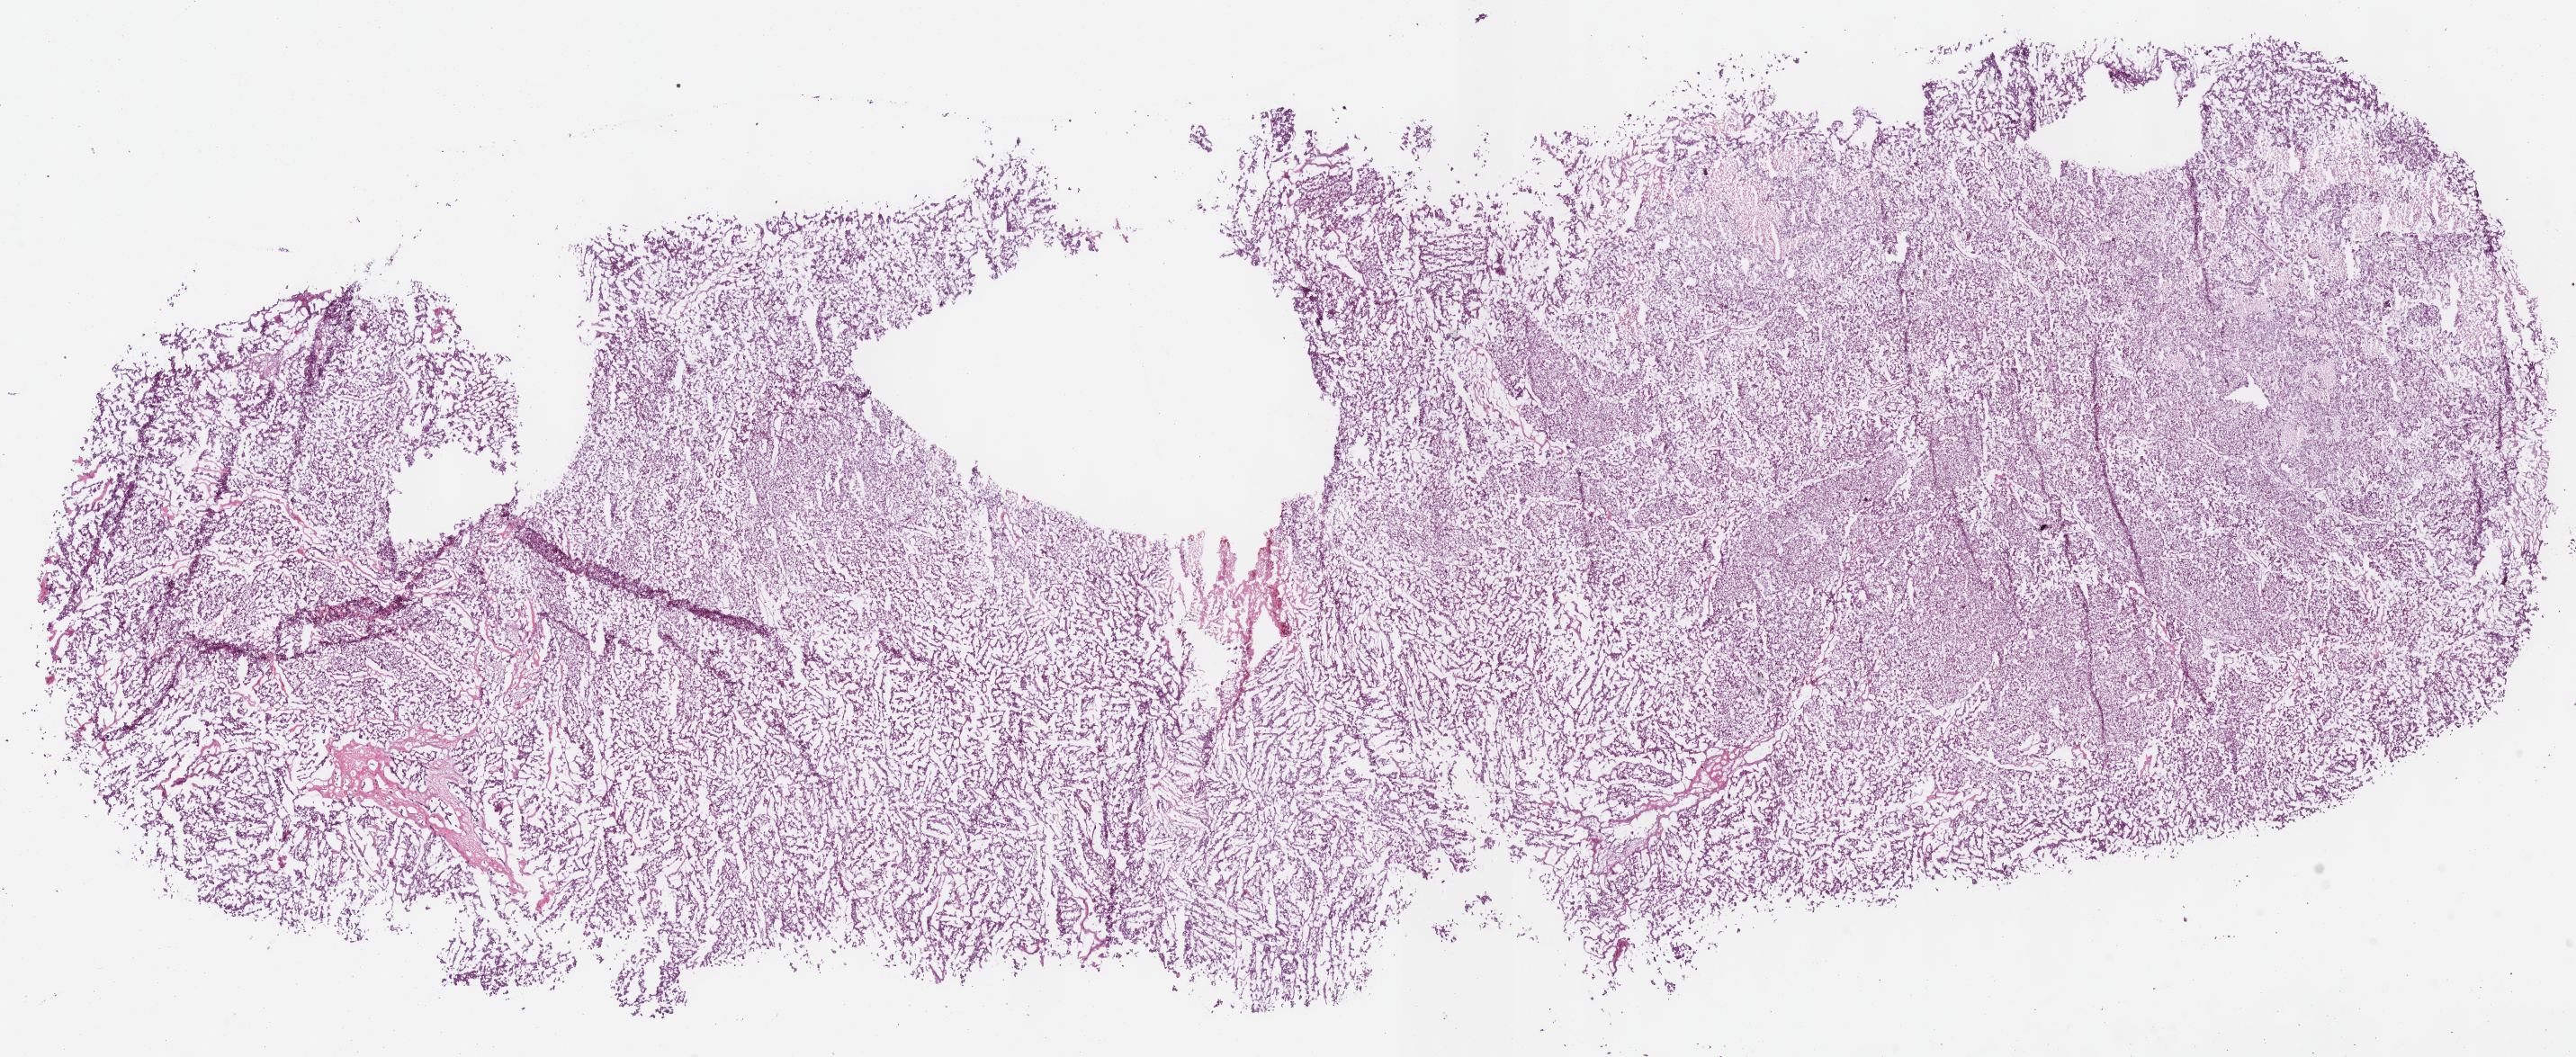
Whole-slide histology image, H&E, whole scanned area (about 22.5 x 9.2 mm) shown as a low-resolution overview, frozen section from the bottom of the tissue portion, primary tumour sample from the kidney. Patient: female, age at initial diagnosis 44 years. Slide review estimates, as recorded: tumour cells 90%, tumour nuclei 90%, normal cells 0%, stromal cells 10%, necrosis 0%.
* AJCC pathologic stage: I (7th edition)
* diagnosis: Renal cell carcinoma, chromophobe type
* laterality: right